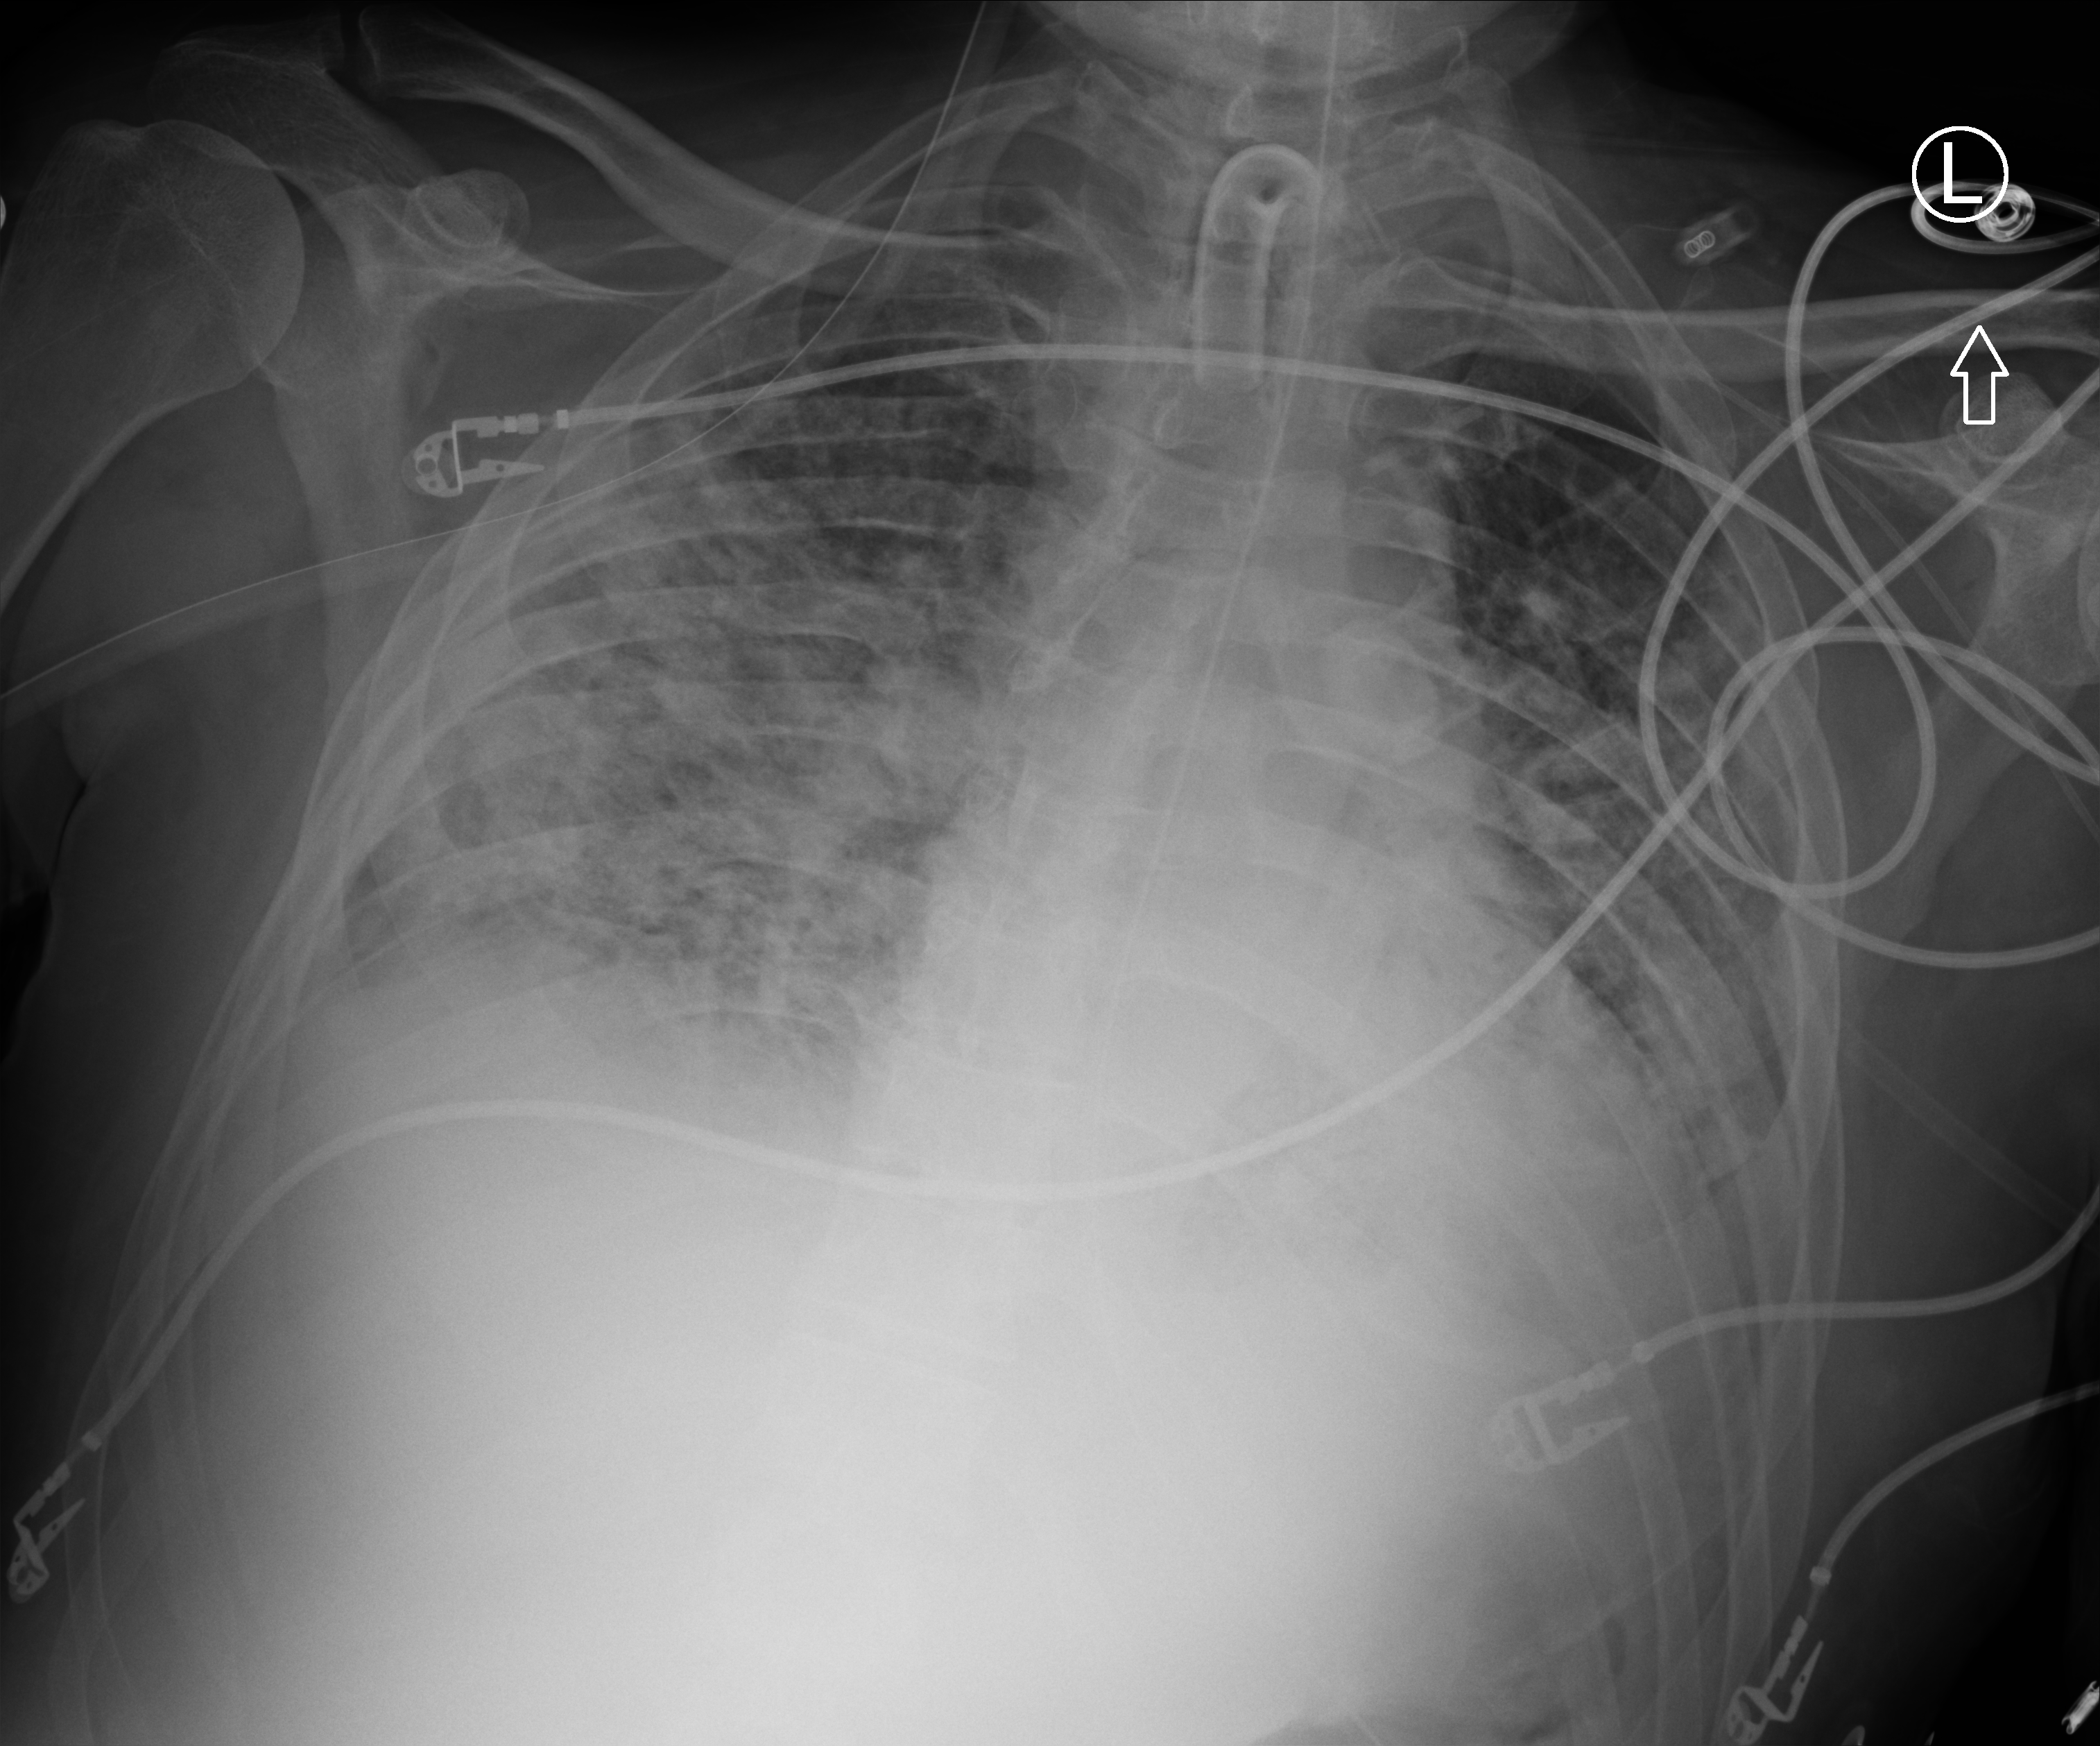
Portable chest radiograph, anteroposterior (AP) projection. Patient hospitalised with COVID-19; male, aged 18–59 years.
Admission-level facts for this patient (not findings on this image; timing relative to this image not recorded):
- mechanically ventilated during this hospital stay: yes
- admitted to intensive care during this hospital stay: yes
- hypertension (admission record): no